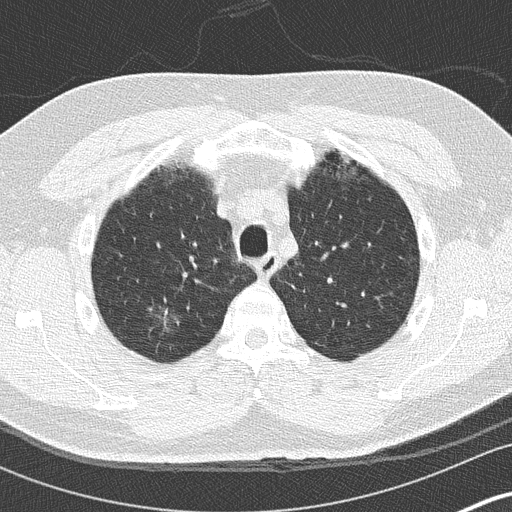
Low-dose screening chest CT, axial slice; first (baseline) screen; lung window (W 1500 / L -600 HU); 2 mm slice thickness; 512 × 512 image matrix, field of view 310 × 310 mm. Male participant, aged 59 years at enrolment. Current smoker at enrolment.
Expert-annotated lung lesion, bounding box <142,292,193,342> (left, top, right, bottom; pixels). Reader record for this screening exam (exam-level; its link to the box is not recorded): non-calcified nodule or mass ≥4 mm, right upper lobe, 16 × 16 mm, ground glass attenuation. Official screen result: positive, change unspecified: nodule(s) >= 4 mm or enlarging nodule(s), mass(es), or other non-specific abnormalities suspicious for lung cancer. Later outcome: lung cancer diagnosed 456 days after this screen (after the second annual screen) — bronchiolo-alveolar adenocarcinoma, NOS, right lower lobe, stage IA (AJCC 6th edition), 15 mm at pathology.